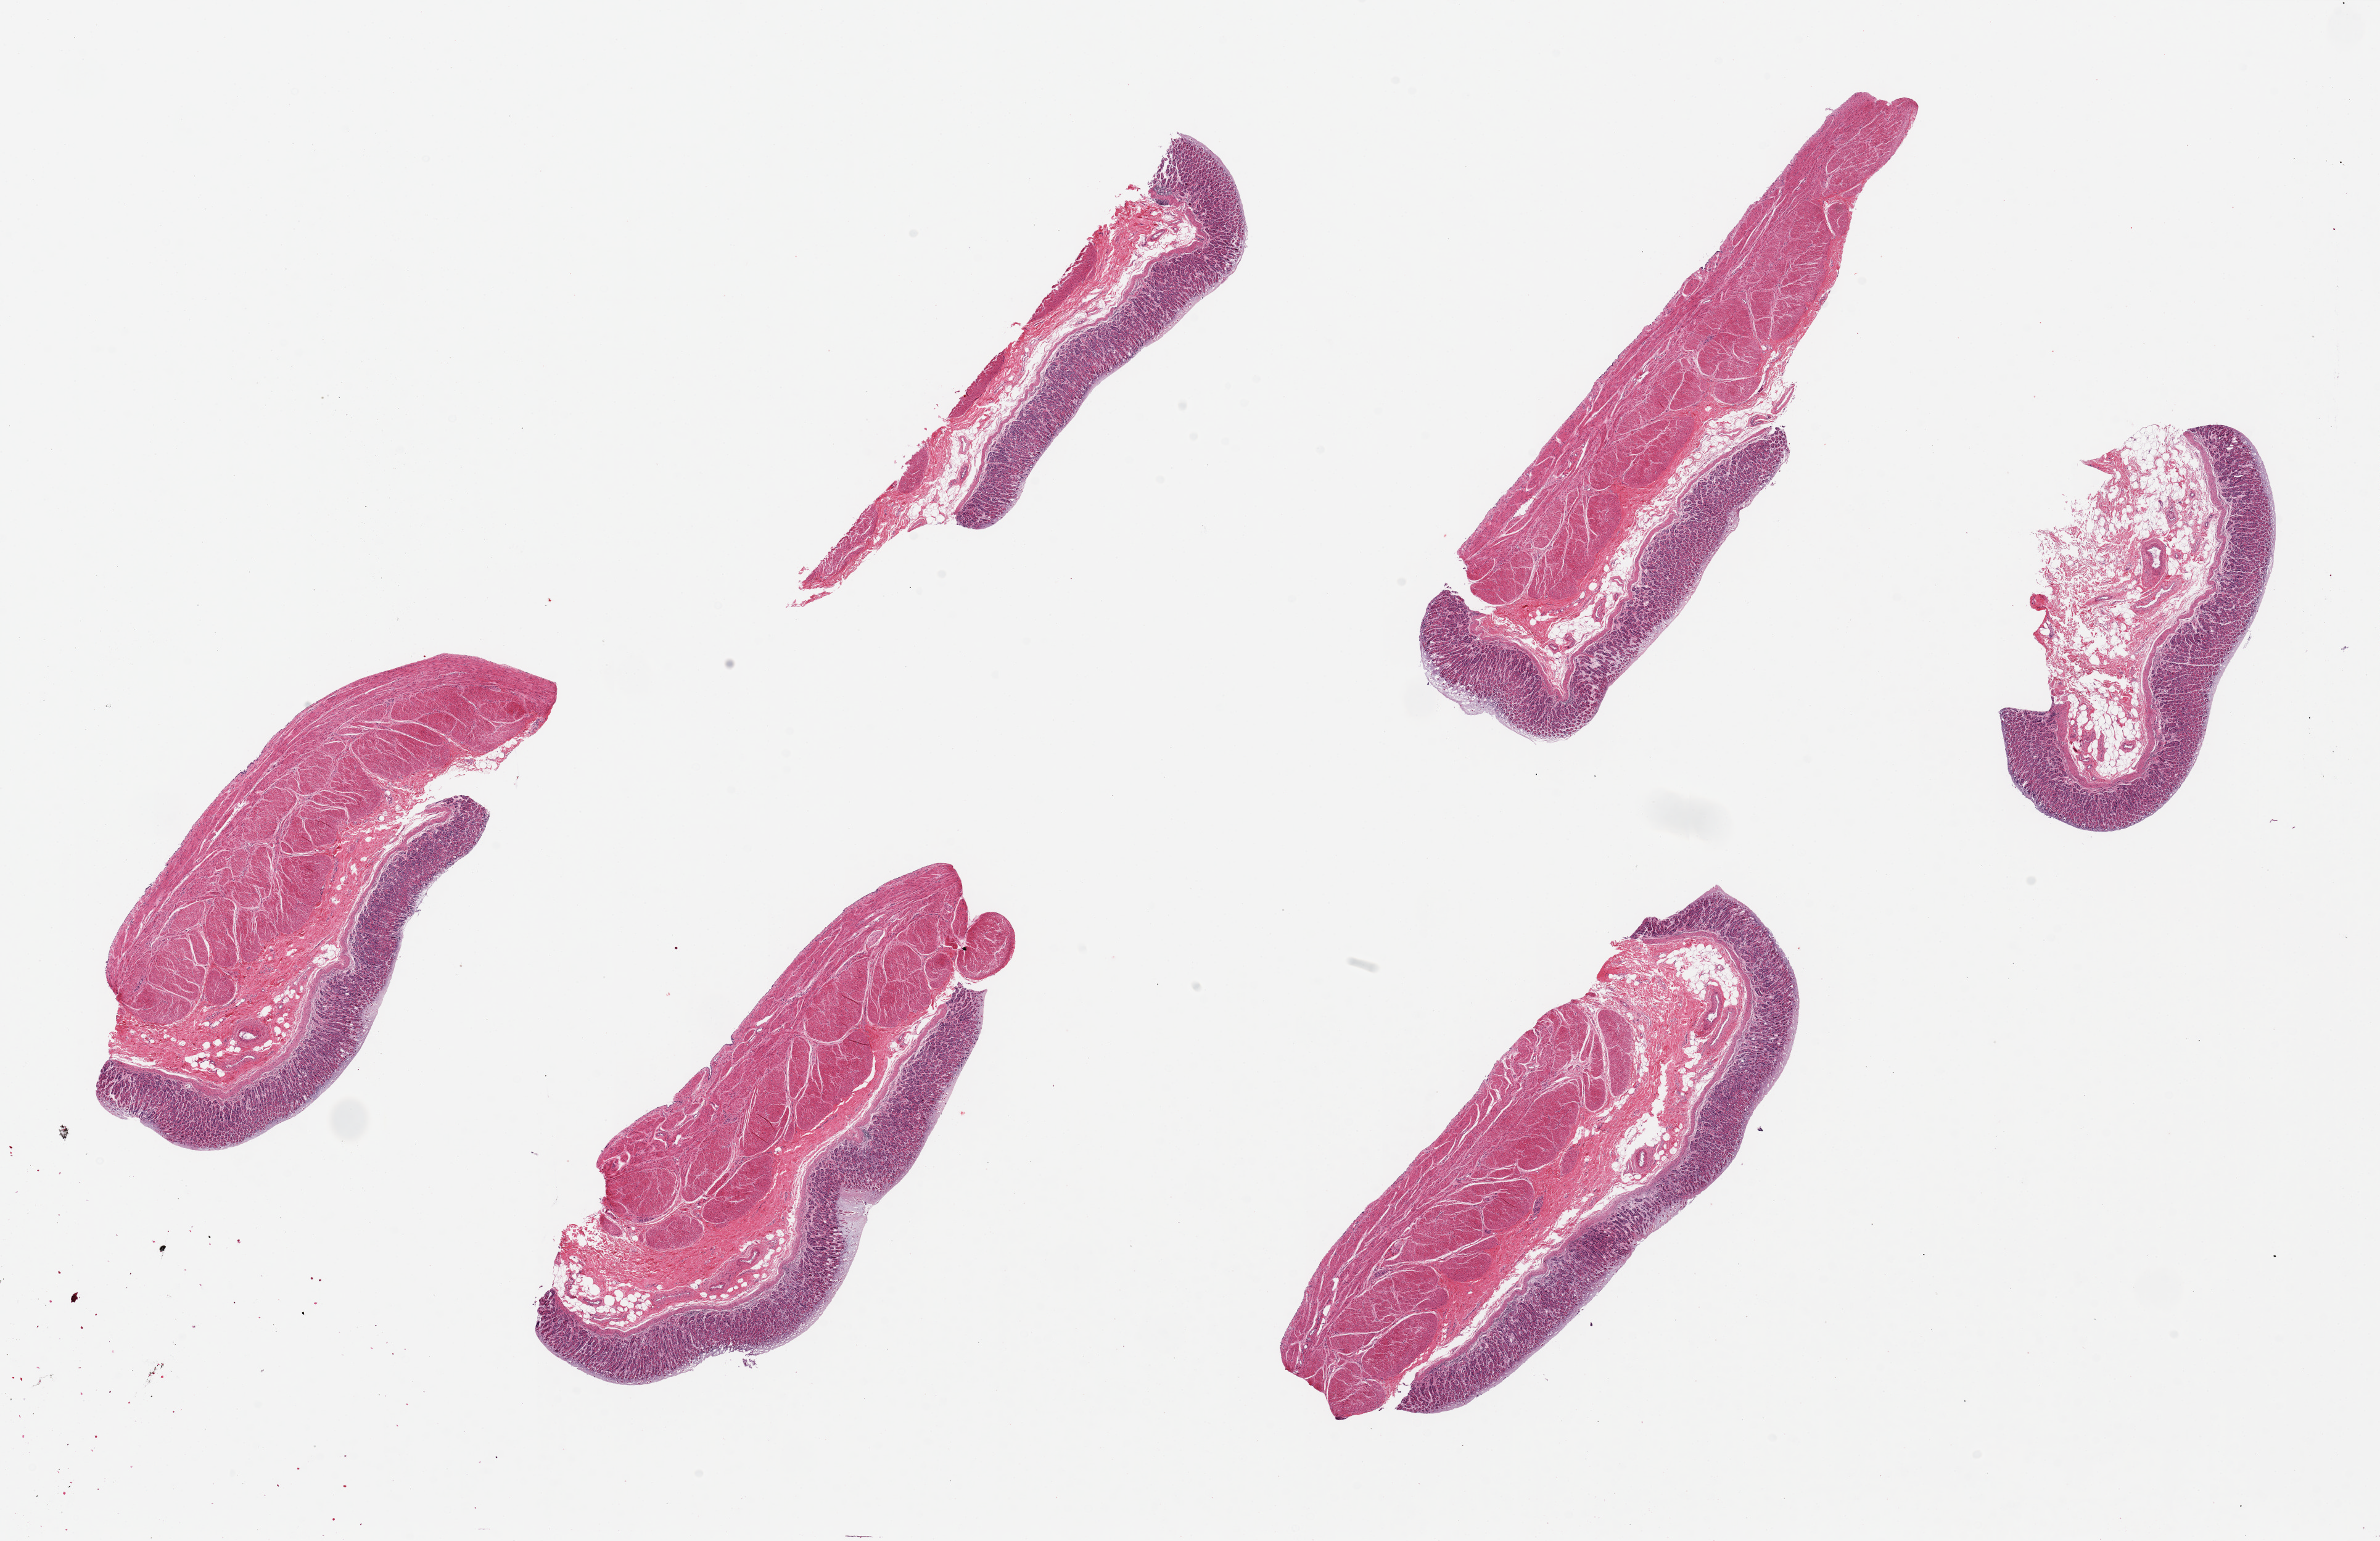
Whole-slide image, hematoxylin and eosin (H&E) stain — low-resolution overview of the scanned area, about 30.5 x 19.8 mm (slide scanned at 20x), PAXgene-fixed paraffin-embedded (PFPE) section, target tissue: stomach, tissue donor sample. Donor: male.
Reviewer comment on this tissue sample: 6 pieces, ~8x3mm Mucosa moderate autolyzed, ~25% thickness.